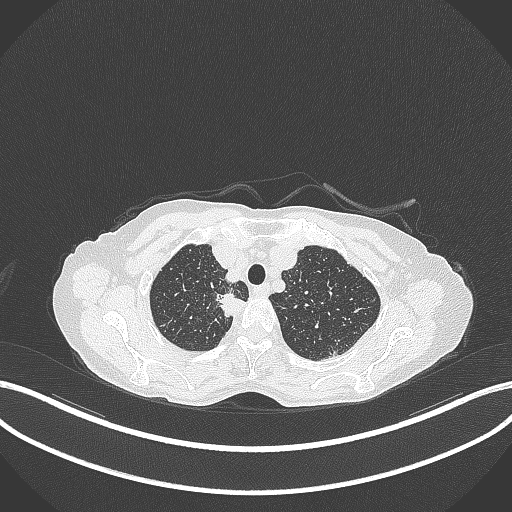
Chest CT, one axial slice; slice 316 of 403 in the series (ordered by position); reconstruction kernel B70f; 120 kVp; lung window (W 1500 / L -600 HU); 512 × 512 image matrix. Female patient, age 75 years. Case-level facts recorded for this patient, not image findings: clinical TNM (as recorded): T1c N1 M1.
Outlined on this slice (rectangle marked by the reading radiologist):
- lung tumour (recorded histology: adenocarcinoma): bounding box [x1, y1, x2, y2] px = [214, 293, 247, 321]